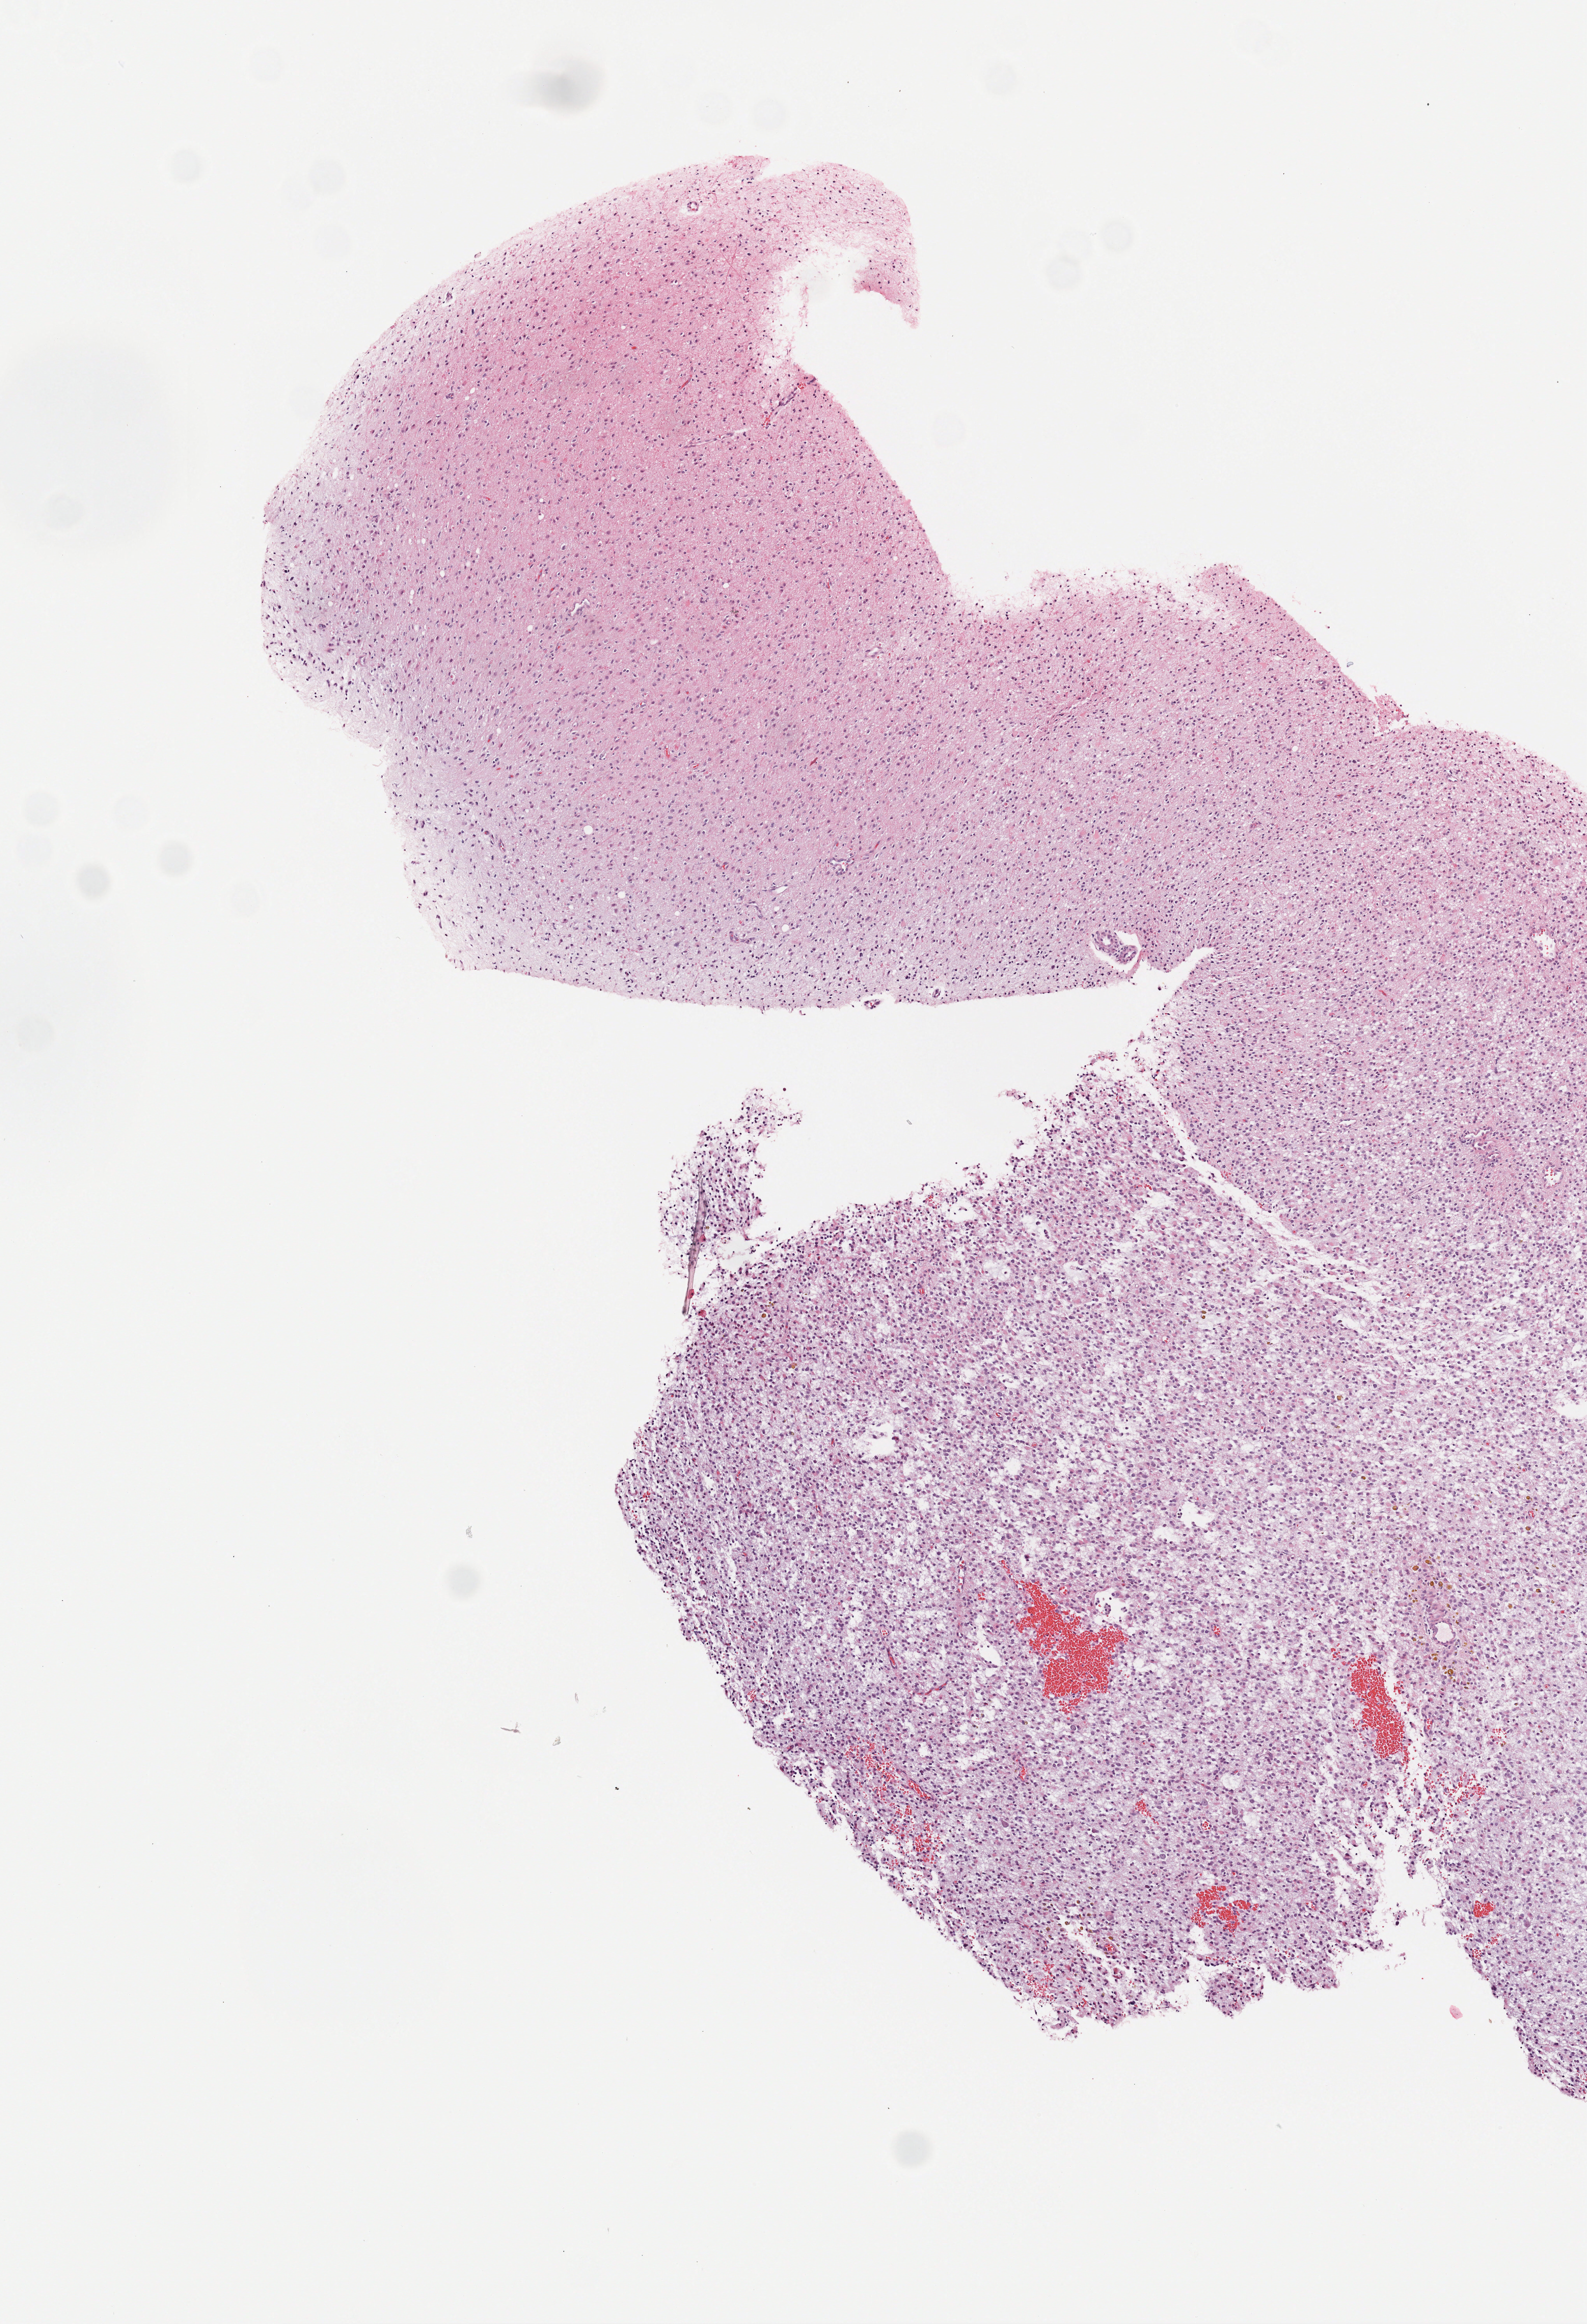
H&E-stained whole-slide image, a low-resolution overview of the entire scanned area, about 4.1 x 6.0 mm (slide scanned at 40x). Formalin-fixed paraffin-embedded (FFPE) diagnostic section. Sample: primary tumour, brain. Male patient; age at initial diagnosis 29 years. Histologic grade: G3 (poorly differentiated).
Laterality: left. Pathologic diagnosis: Mixed glioma.